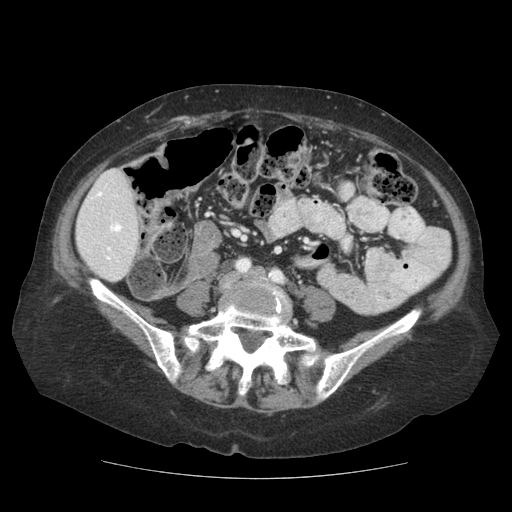
Contrast-enhanced abdominal CT (liver protocol), one axial slice. Slice 25 of 111 in the series (ordered by position). Reconstruction kernel STANDARD. 140 kVp. Soft-tissue window (W 400 / L 40 HU). 2.5 mm slice thickness. 512 × 512 image matrix, field of view 360 × 360 mm. From the clinical record (not read from this slice): diagnosis: hepatocellular carcinoma (patient treated with transarterial chemoembolisation; whether this scan precedes or follows treatment is not stated here); TNM stage (as recorded): Stage-I; Child-Pugh class: A; tumour nodularity: uninodular; tumour size: 7.3 cm.
Structures marked on this image (semi-automatically segmented with operator editing):
- liver parenchyma outside the tumour (the mass and vessels are separate outlines, so this box may not span the whole liver): bounding box (x1, y1, x2, y2) in pixels: (76, 168, 138, 282)
- liver vessels: (97, 192, 122, 260)